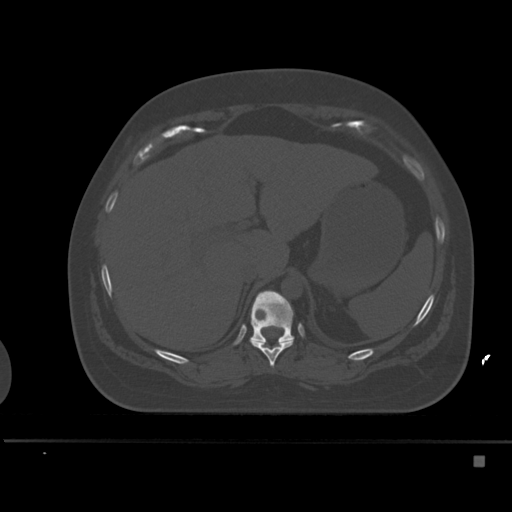
CT including the spine, one axial slice. Bone window (W 1800 / L 400 HU). 1.5 mm slice thickness. 512 × 512 image matrix, field of view 404 × 404 mm. Female patient, age 33 years. Case-level facts recorded for this patient, not image findings: primary cancer: breast; vertebrae with lytic lesions (as recorded): T1.
Outlined on this slice (semi-automatically segmented with operator editing):
- T10 vertebra: bounding box [x1, y1, x2, y2] px = [250, 340, 294, 368]
- T11 vertebra: [250, 290, 294, 343]